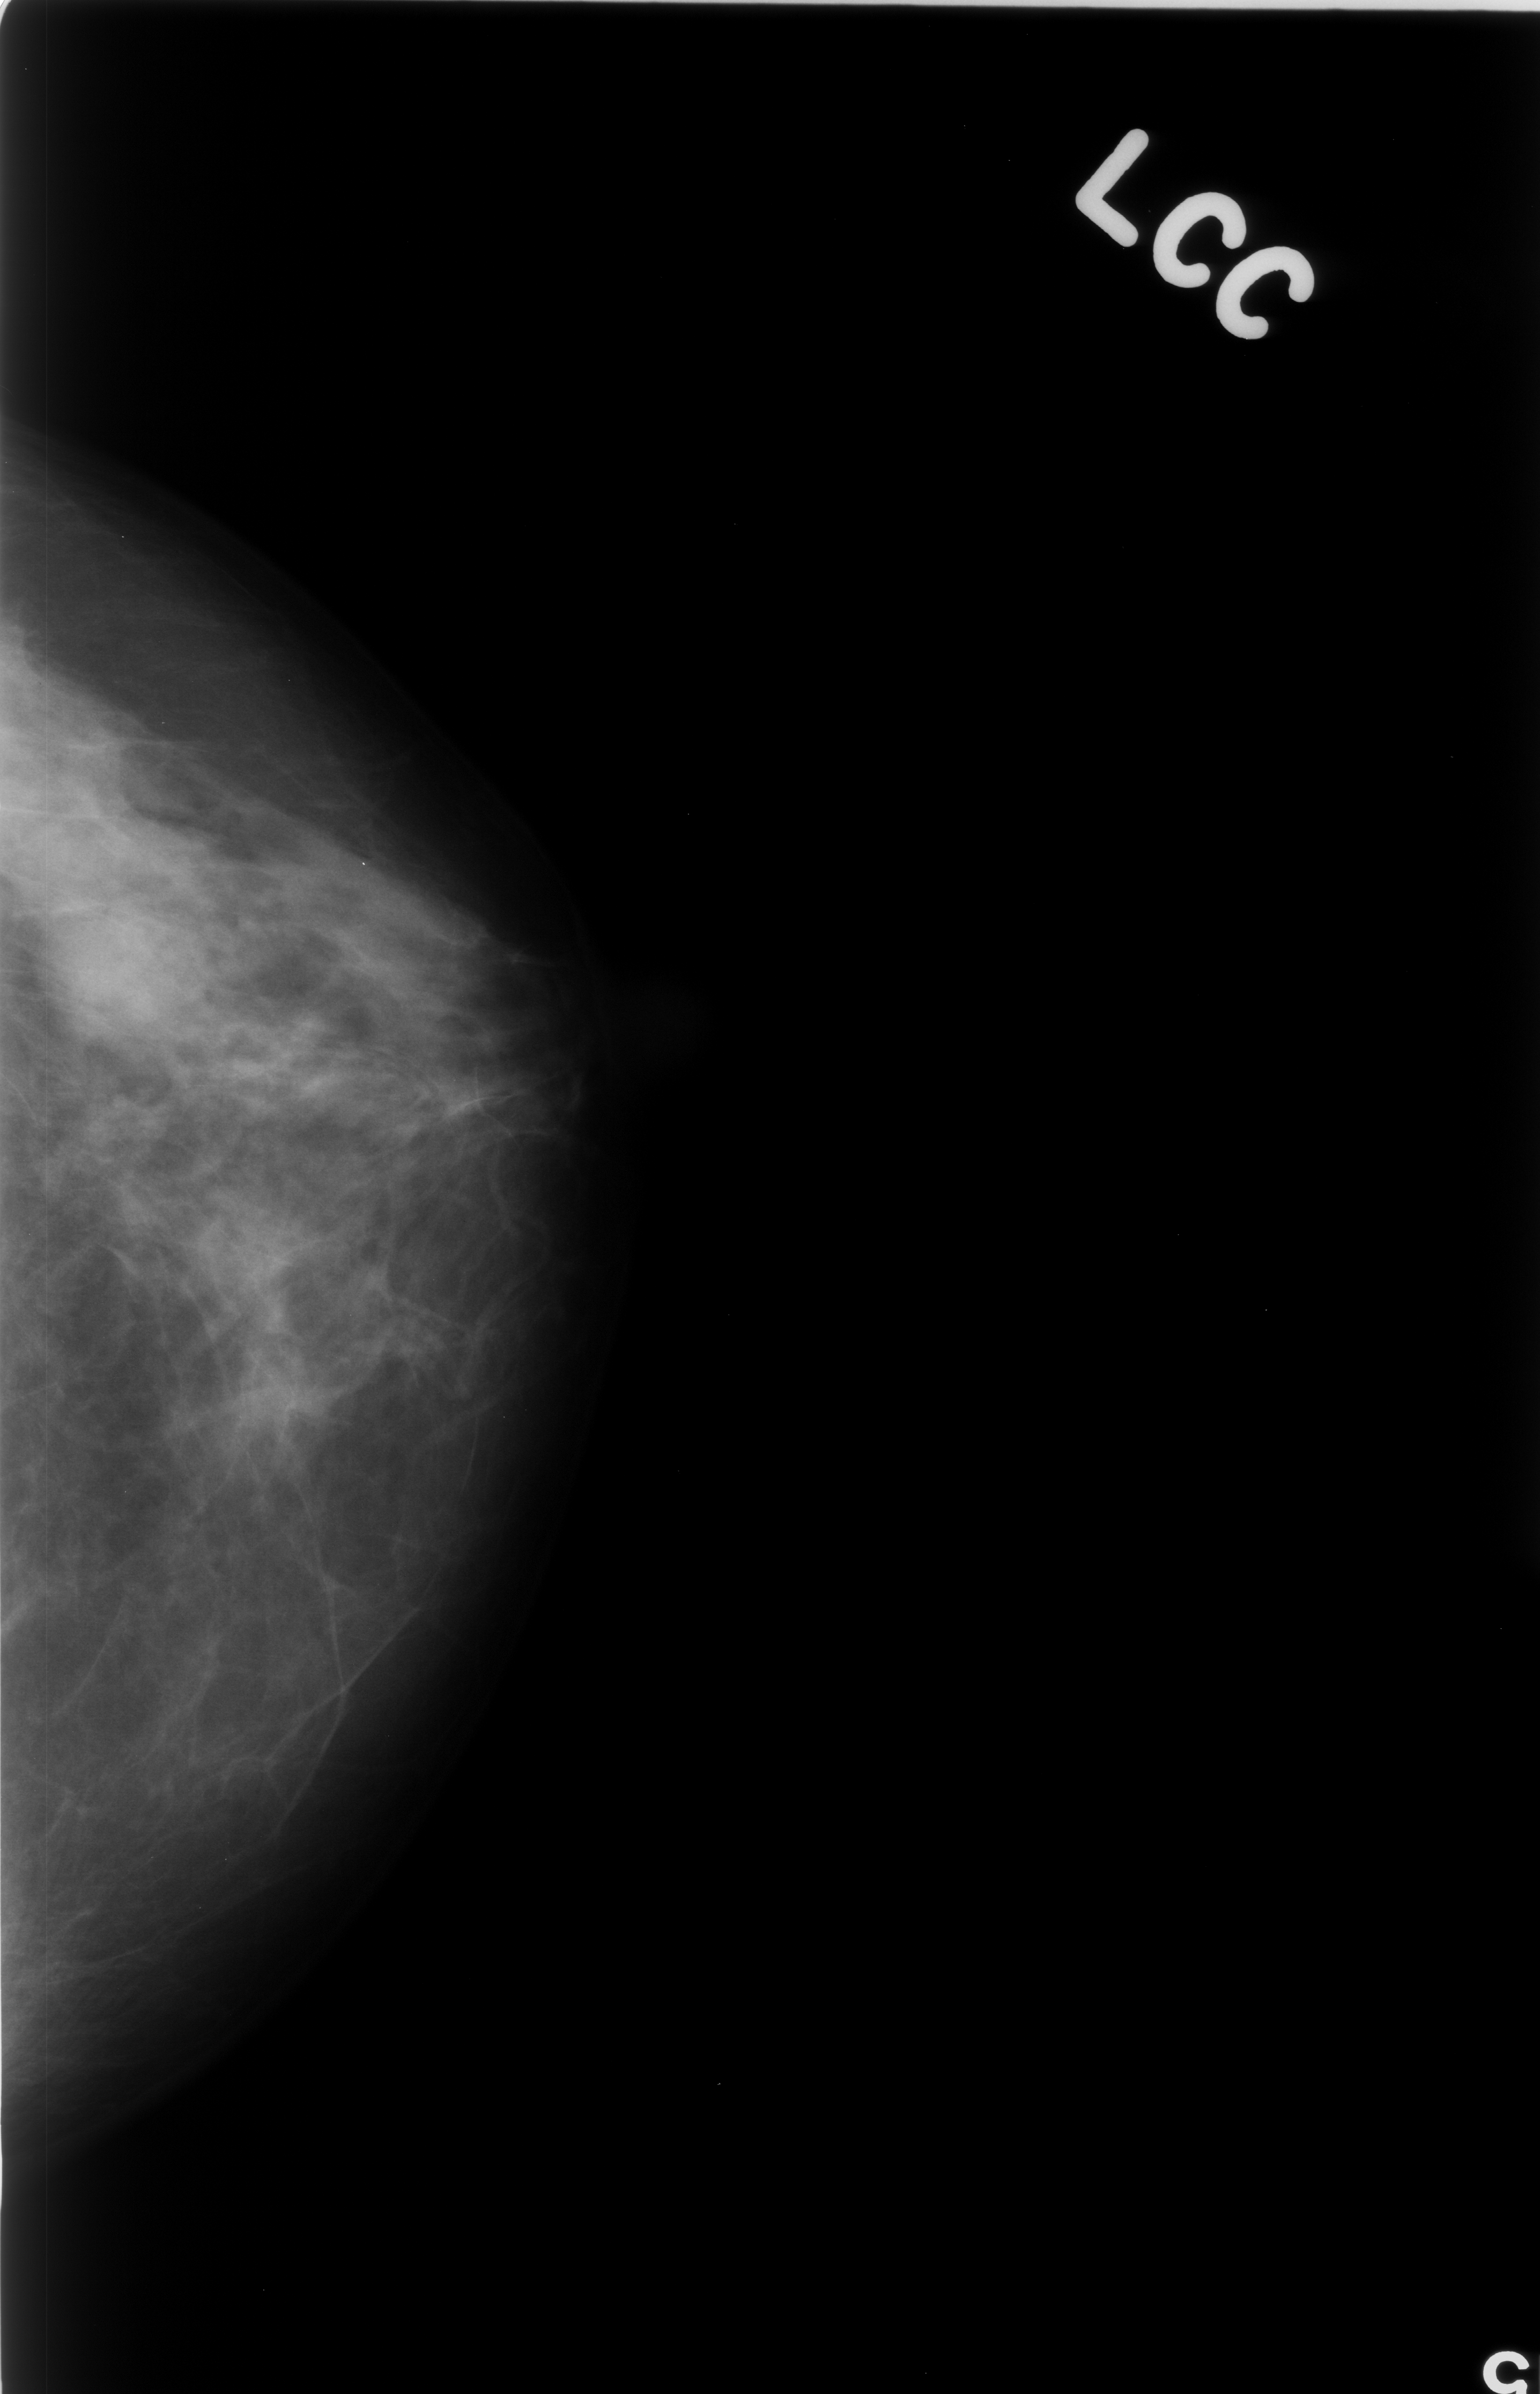
Digitized screen-film mammogram, left breast, craniocaudal (CC) view, breast composition: scattered fibroglandular densities (BI-RADS density category 2 of 4).
Marked findings (only marked abnormalities are described; nothing is implied about the rest of the image): mass, shape oval, margins obscured; BI-RADS assessment category 4; pathology result (as recorded, not read from the image): benign.